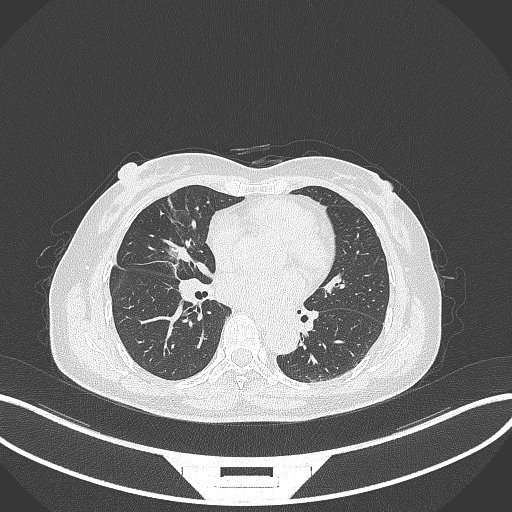
Chest CT, one axial slice. Slice 140 of 284 in the series (ordered by position). Reconstruction kernel B70f. Lung window (W 1500 / L -600 HU). 1 mm slice thickness. 512 × 512 image matrix, field of view 400 × 400 mm. Female patient, age 51 years. From the clinical record (not read from this slice): clinical TNM (as recorded): T1c N0 M0.
Annotated regions visible in this slice (bounding box drawn by a radiologist):
- lung tumour (recorded histology: adenocarcinoma): bounding box <159,232,192,272> (left, top, right, bottom; pixels)